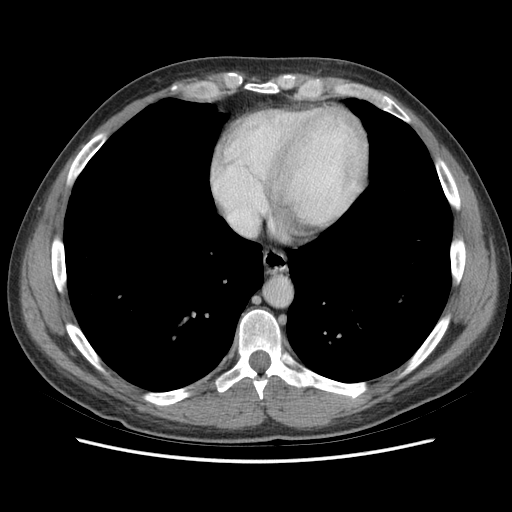
Contrast-enhanced abdominal CT (liver protocol), one axial slice. Position 72 of 73 along the scan axis. Soft-tissue window (W 400 / L 40 HU). 2.5 mm slice thickness. 512 × 512 image matrix. From the clinical record (not read from this slice): diagnosis: hepatocellular carcinoma (patient treated with transarterial chemoembolisation; whether this scan precedes or follows treatment is not stated here); TNM stage (as recorded): Stage-IIIA; Child-Pugh class: A; tumour nodularity: multinodular; tumour size: 6.6 cm.
Outlined on this slice (semi-automatically segmented with operator editing):
- abdominal aorta: bounding box <264,278,291,306> (left, top, right, bottom; pixels)